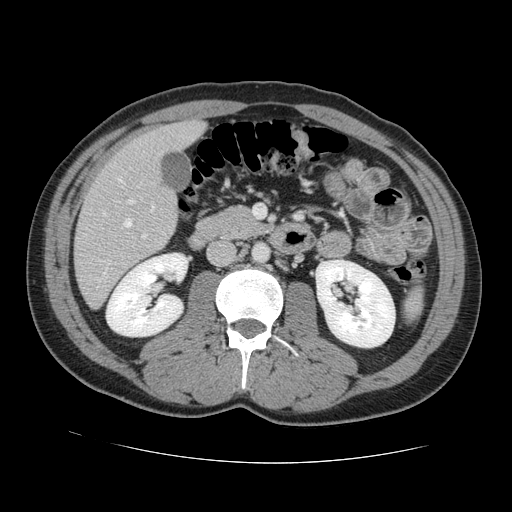
Contrast-enhanced abdominal CT, one axial slice. 120 kVp. Intravenous contrast given. Soft-tissue window (W 400 / L 40 HU). 512 × 512 image matrix. Male patient, age 40 years. Case-level facts recorded for this patient, not image findings: diagnosis: colorectal cancer liver metastases, imaged before liver resection; multiple liver metastases: yes; largest metastasis: 2.9 cm; chemotherapy before resection: yes.
Structures marked on this image (outlined manually by an expert reader):
- hepatic veins: bounding box <103,179,153,227> (left, top, right, bottom; pixels)
- liver: <75,123,203,307>
- planned liver remnant (the part of the liver to remain after resection): <120,123,204,170>
- portal vein (with intrahepatic branches): <128,199,147,238>